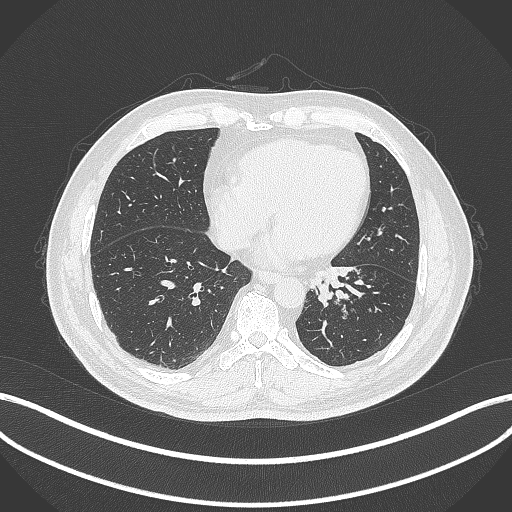
Chest CT, one axial slice. Position 88 of 312 along the scan axis. Lung window (W 1500 / L -600 HU). 1 mm slice thickness. 512 × 512 image matrix, field of view 400 × 400 mm. Male patient, age 71 years. From the clinical record (not read from this slice): clinical TNM (as recorded): T1b N0 M0.
Annotated regions visible in this slice (rectangle marked by the reading radiologist):
- lung tumour (recorded histology: squamous cell carcinoma): bounding box <310,263,363,308> (left, top, right, bottom; pixels)